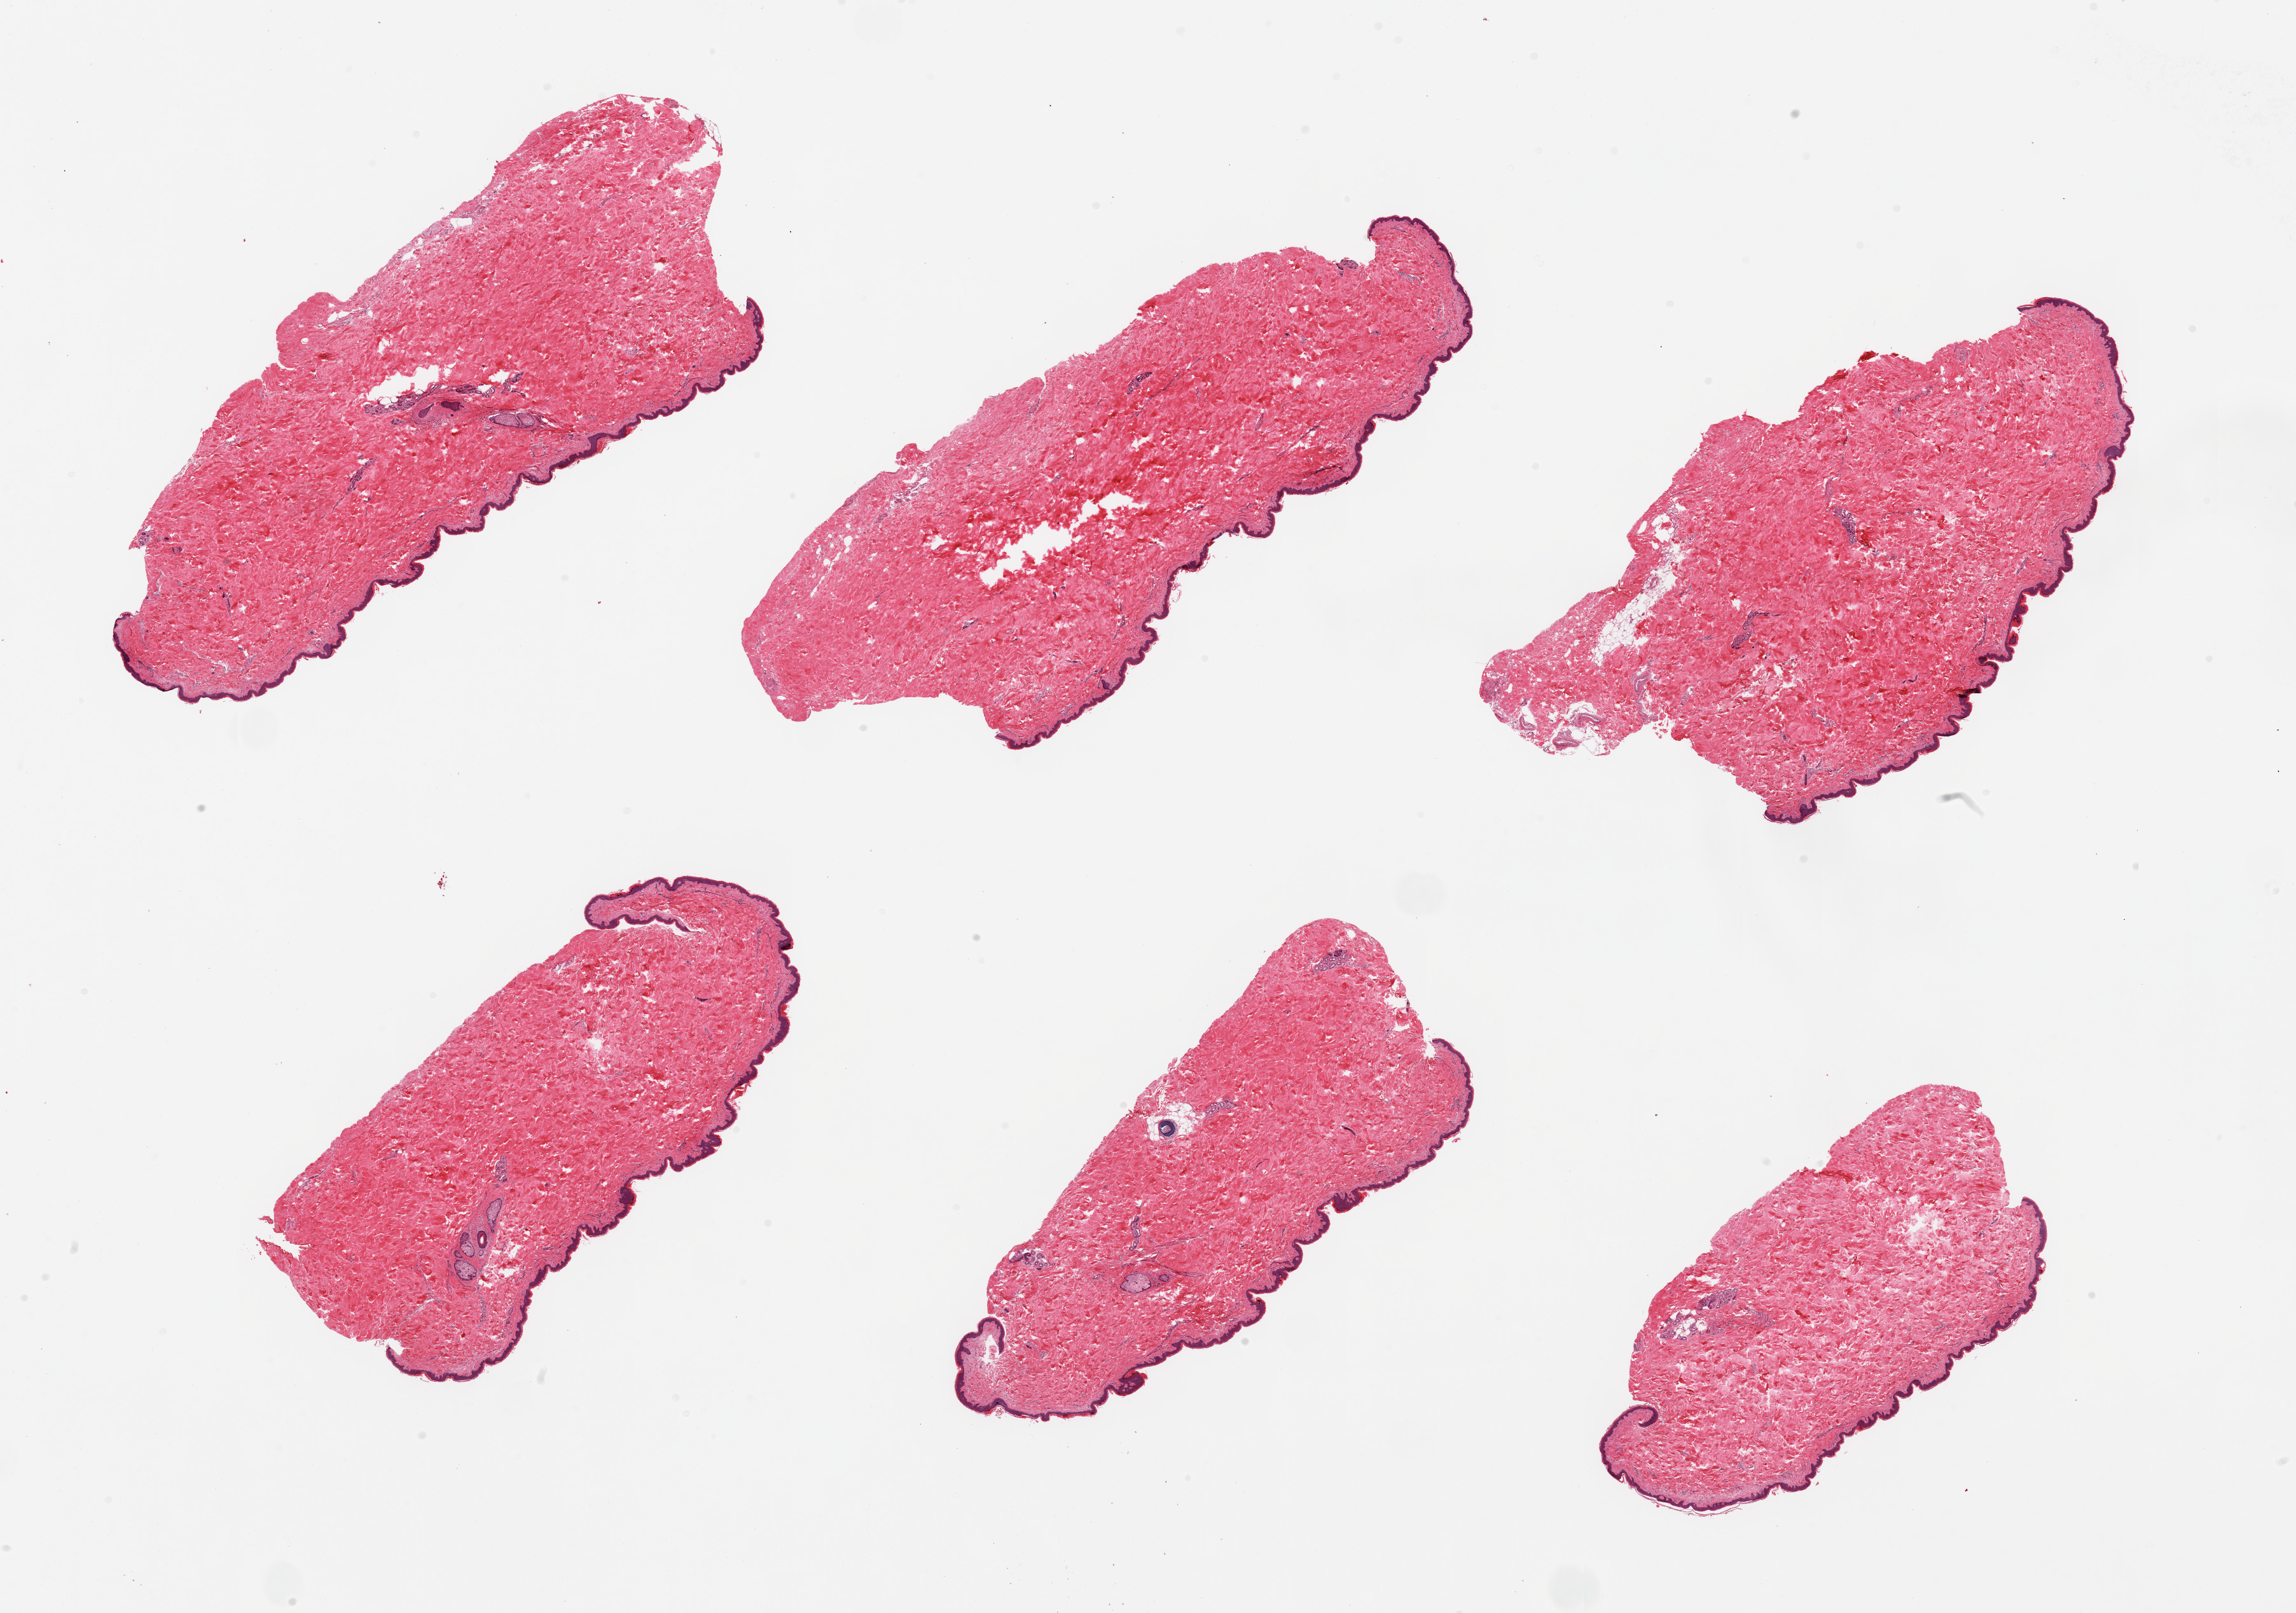
Whole-slide image, hematoxylin and eosin (H&E) stain, whole scanned area (about 28.5 x 20.1 mm, acquisition: 20x scan) shown as a low-resolution overview; PAXgene-fixed paraffin-embedded (PFPE) section; target tissue: skin of suprapubic region; donor tissue sample. Donor sex: male.
Pathologist's review note for this sample: 6 pieces; minimal amount of periadnexal fat.